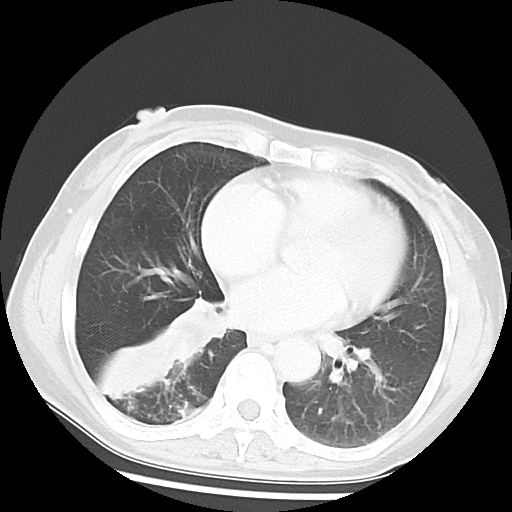
Chest CT, one axial slice. Slice 24 of 52 in the series (ordered by position). Reconstruction kernel LUNG. 120 kVp. Lung window (W 1500 / L -600 HU). 512 × 512 image matrix, field of view 297 × 297 mm. Patient: female, 54 years. Case-level facts recorded for this patient, not image findings: clinical TNM (as recorded): T1c N0 M0.
Structures marked on this image (rectangle marked by the reading radiologist):
- lung tumour (recorded histology: squamous cell carcinoma): bounding box <175,291,229,362> (left, top, right, bottom; pixels)